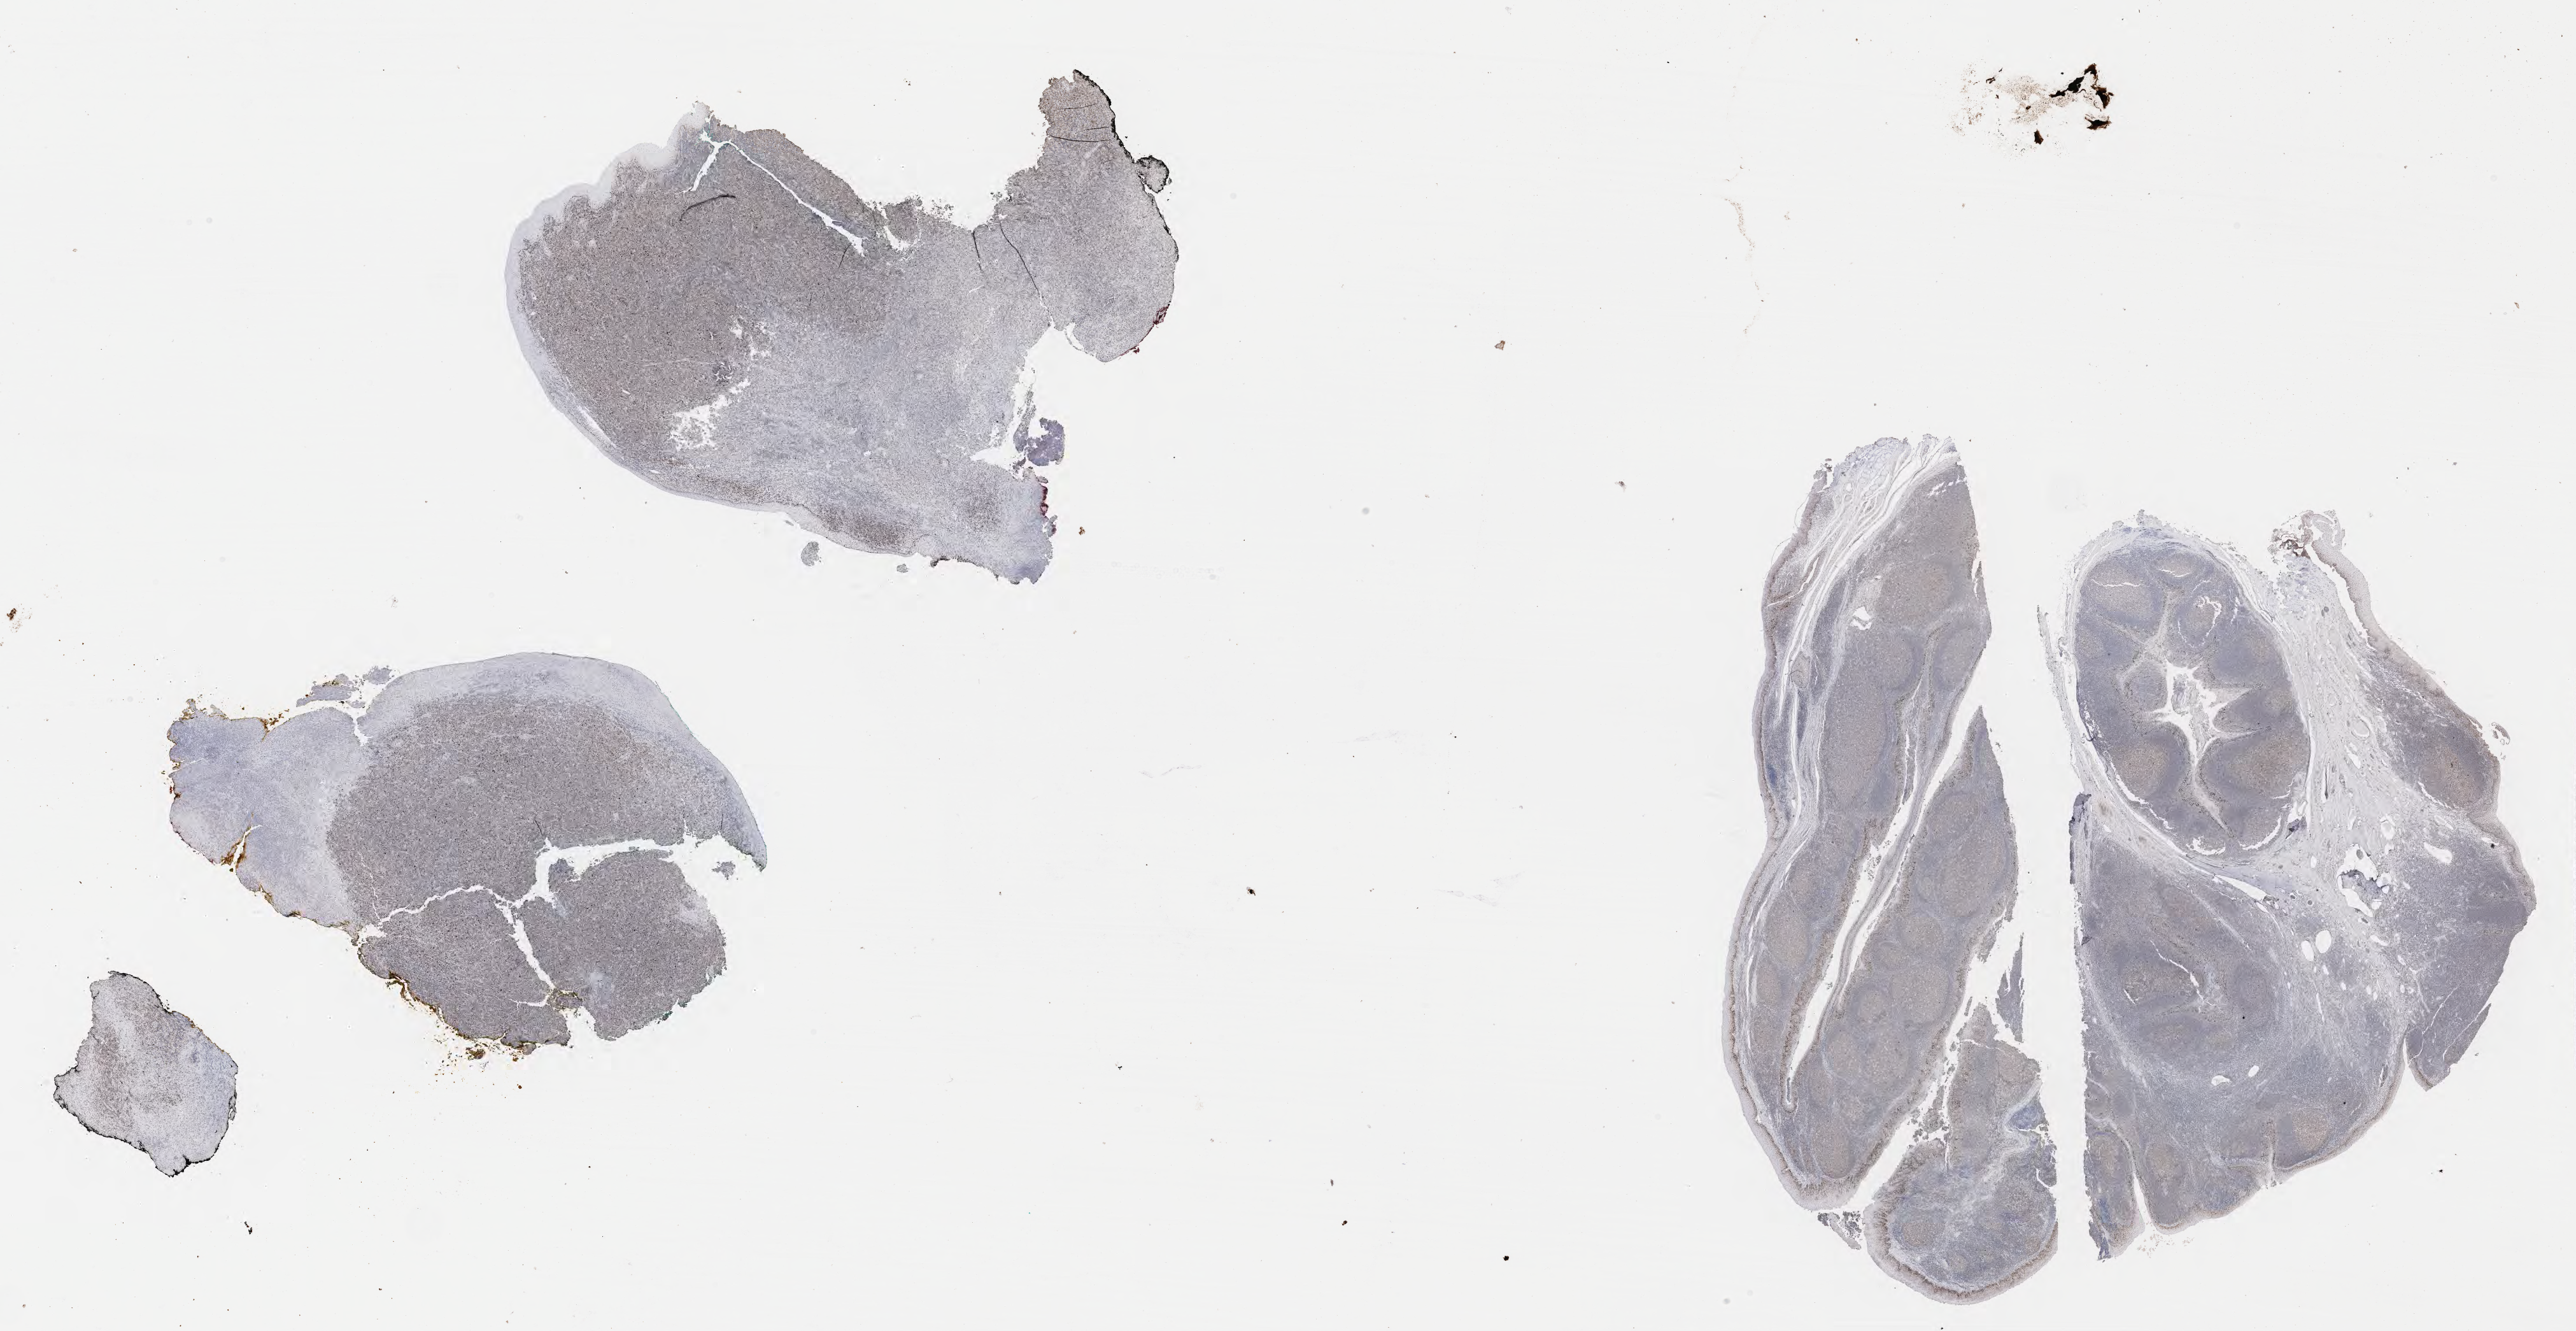
Immunohistochemistry (IHC) whole-slide image stained for p53, whole scanned area (about 32.7 x 16.9 mm) shown as a low-resolution overview, tumor tissue. Patient: male, age 49 years.
• diagnosis: Diffuse large B-cell lymphoma, NOS